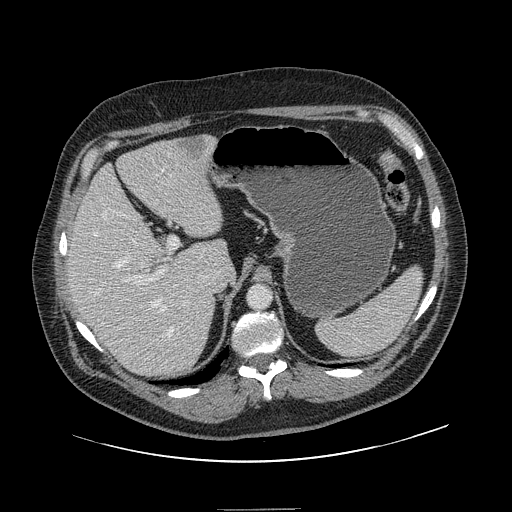
Contrast-enhanced abdominal CT, one axial slice; position 100 of 154 along the scan axis; 120 kVp; intravenous contrast given; soft-tissue window (W 400 / L 40 HU); 512 × 512 image matrix, field of view 451 × 451 mm. Male patient, age 61 years. Case-level facts recorded for this patient, not image findings: diagnosis: colorectal cancer liver metastases, imaged before liver resection; multiple liver metastases: yes; largest metastasis: 2.6 cm.
Outlined on this slice (manually delineated by an expert):
- hepatic veins: bounding box (x1, y1, x2, y2) in pixels: (93, 211, 183, 337)
- liver: (68, 137, 225, 379)
- planned liver remnant (the part of the liver to remain after resection): (68, 144, 227, 361)
- portal vein (with intrahepatic branches): (109, 168, 187, 305)
- liver metastasis: (181, 138, 207, 157)